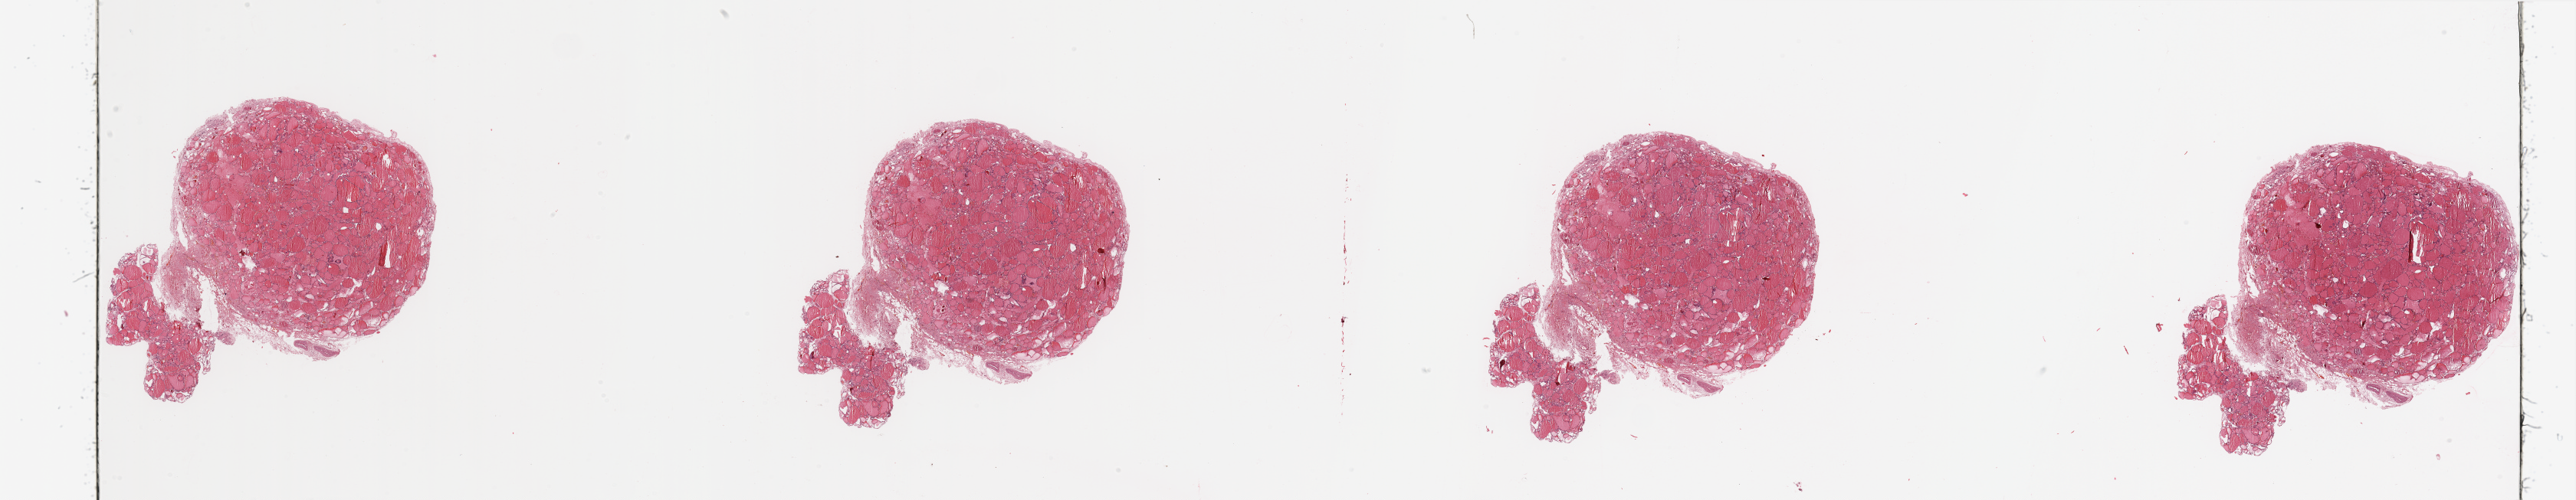
Digitized H&E-stained tissue section (whole slide) — a low-resolution overview of the entire scanned area, about 53.2 x 10.3 mm (acquisition: 20x scan); normal (non-tumour) tissue sample, sampled site: larynx. 81-year-old male patient.
This section: normal (non-tumour) tissue from the same patient. Patient diagnosis: Squamous cell carcinoma, NOS (larynx, NOS).